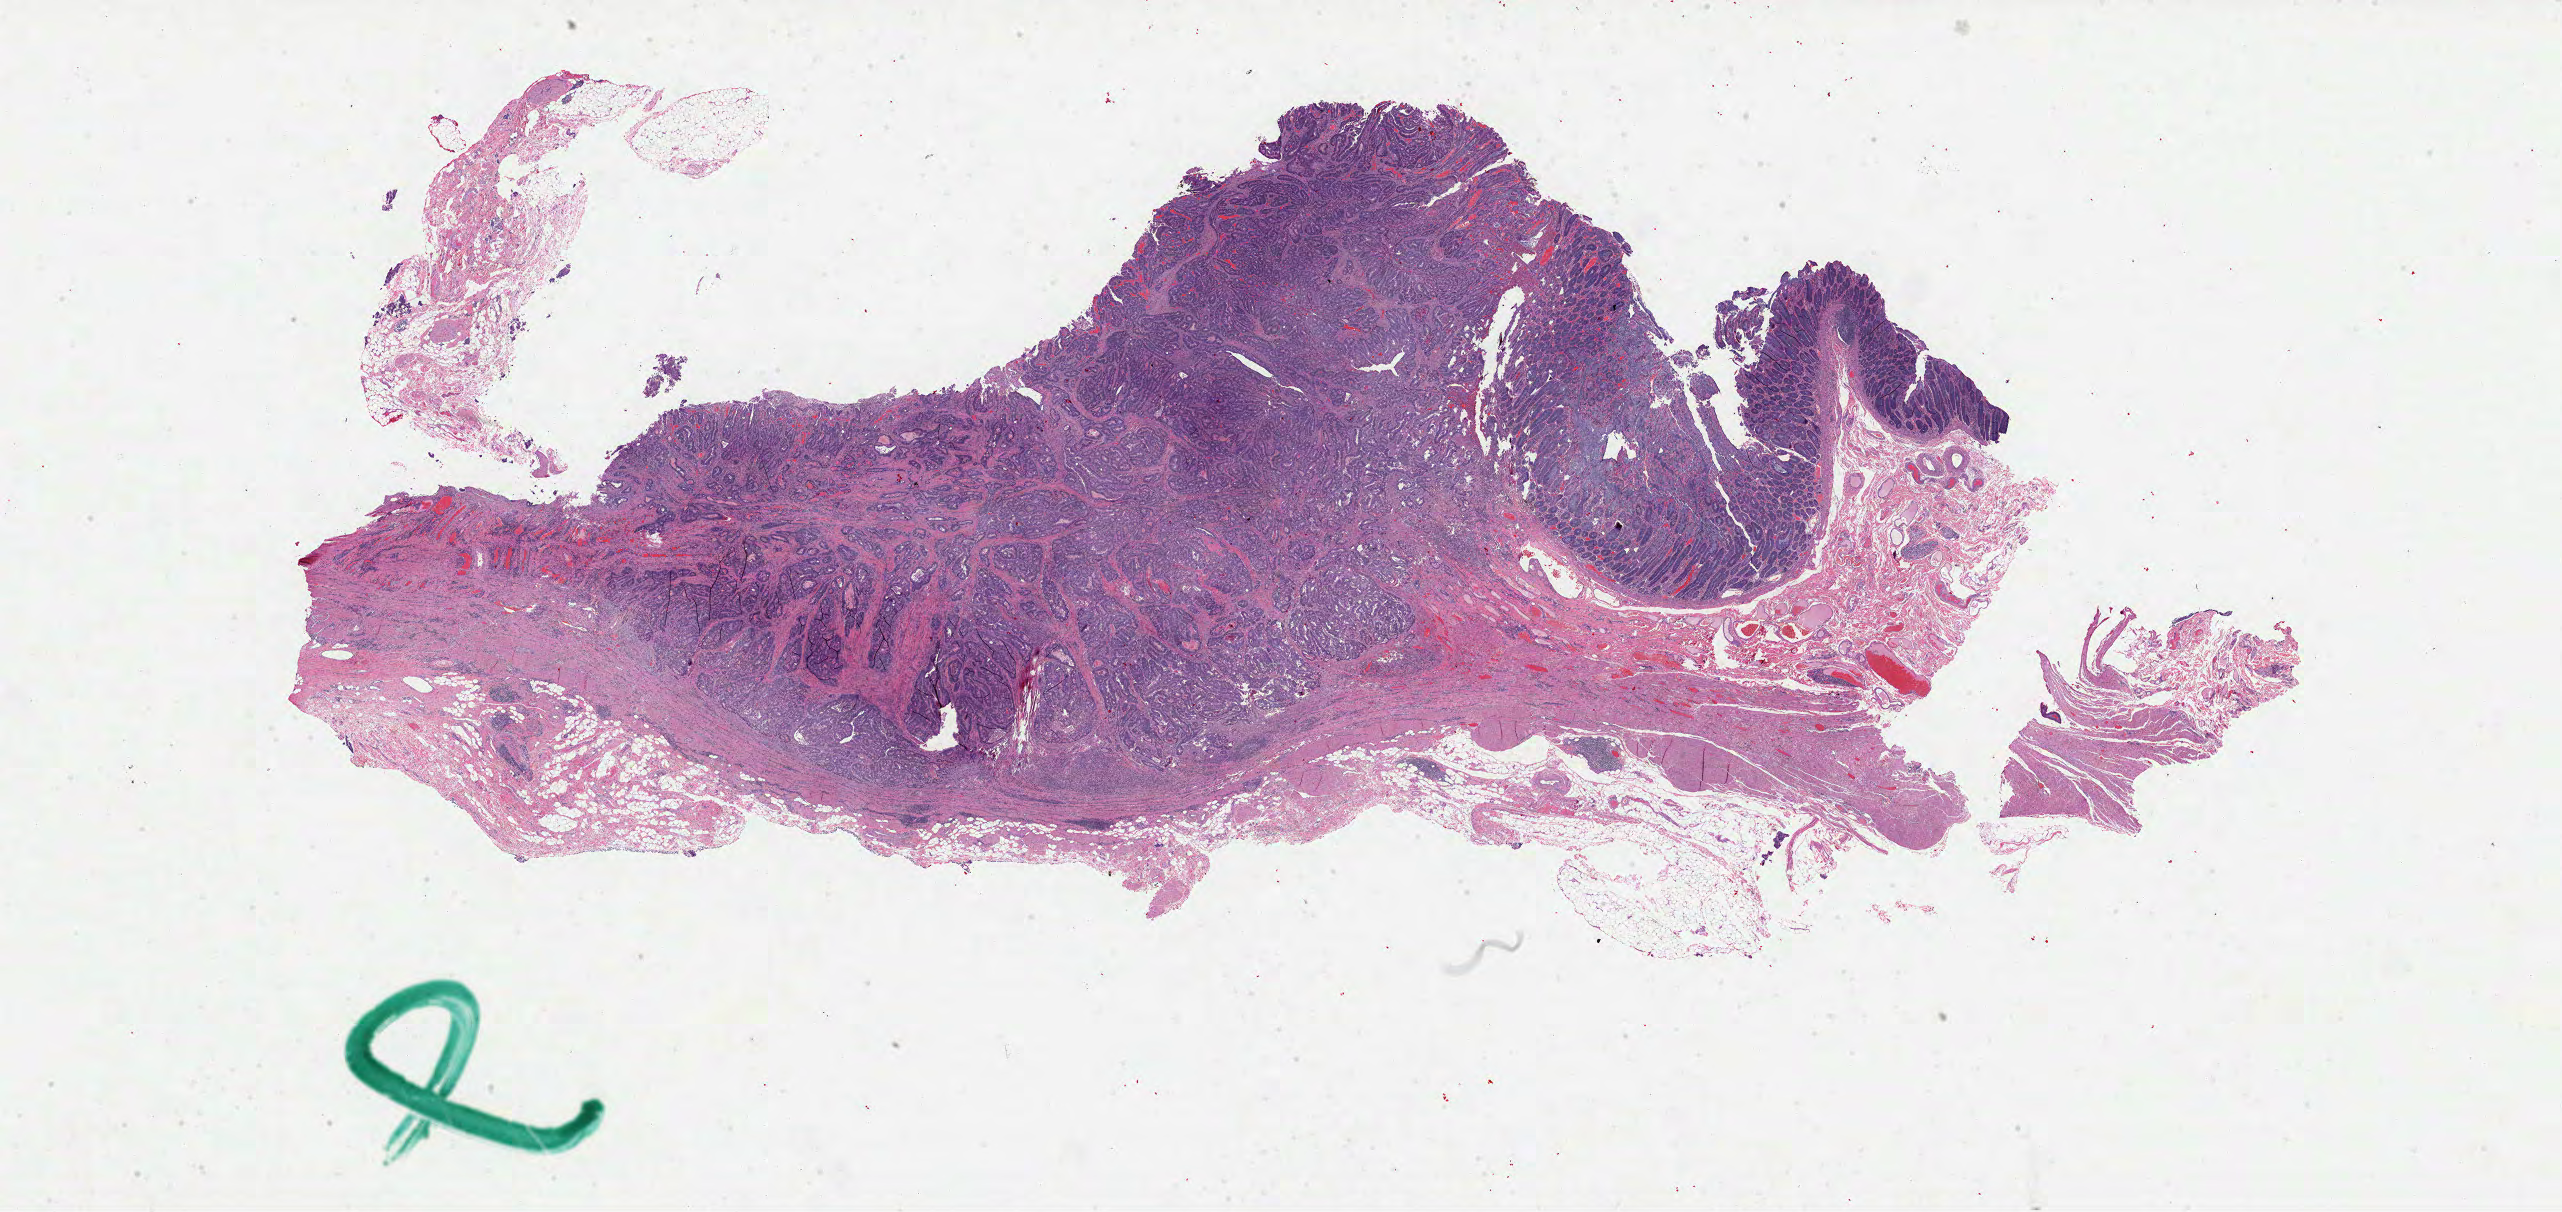
Whole-slide histology image, Hematoxylin and eosin (H&E) stained — whole scanned area (about 41.3 x 19.6 mm, from a 40x scan) shown as a low-resolution overview. Formalin-fixed paraffin-embedded (FFPE) diagnostic section. Colon, primary tumour sample. Patient: male, age at initial diagnosis 60 years.
• lymph nodes positive (case pathology): 0 of 33 examined
• histologic diagnosis: Adenocarcinoma, NOS (cecum)
• AJCC pathologic stage: I